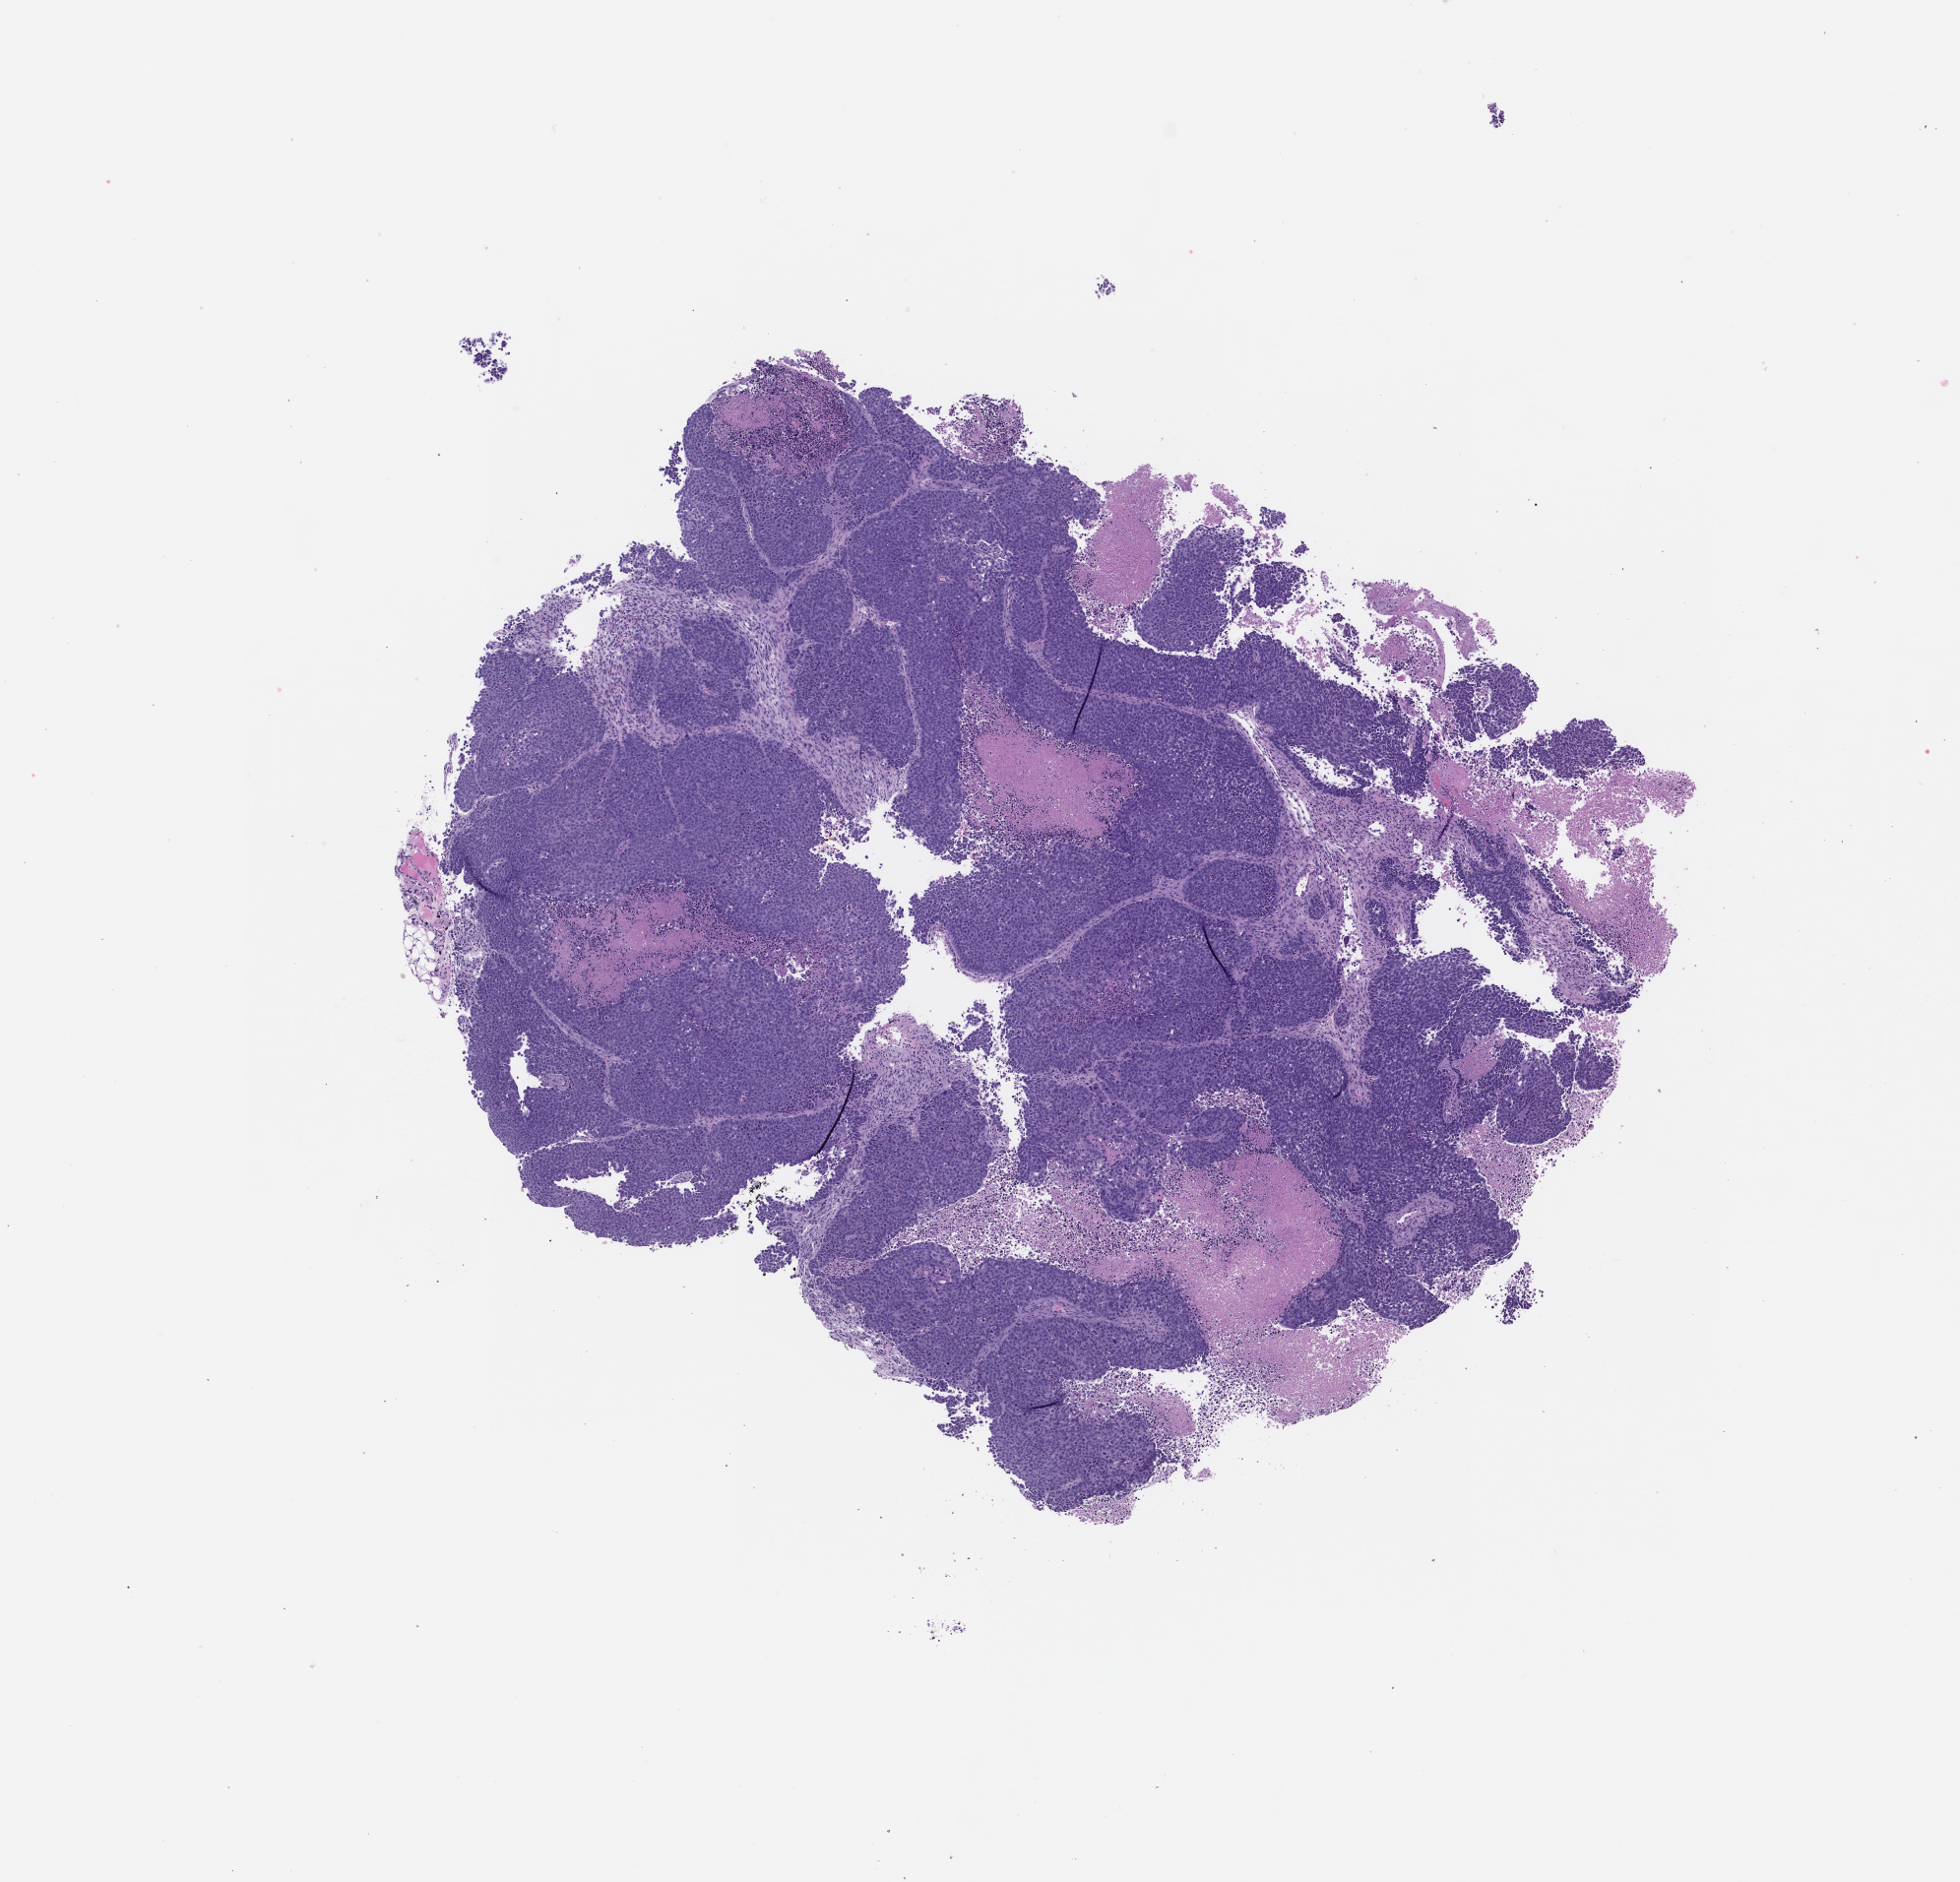
Whole-slide image, H&E: patient-derived xenograft (human tumor grown in a mouse), passage 0 — low-resolution overview of the scanned area, about 8.0 x 7.7 mm. Formalin-fixed, paraffin-embedded (FFPE) tissue. Tumor site category: lung.
• originating patient diagnosis: Lung Squamous Cell Carcinoma